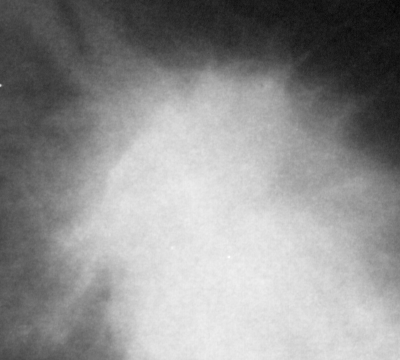
Cropped region of a digitized screen-film mammogram centred on a radiologist-marked abnormality; right breast; CC view.
- Mass, shape irregular, margins spiculated; BI-RADS assessment category 5; subtlety rating 5 on a 1 (subtle) to 5 (obvious) scale; pathology (as recorded): malignant.